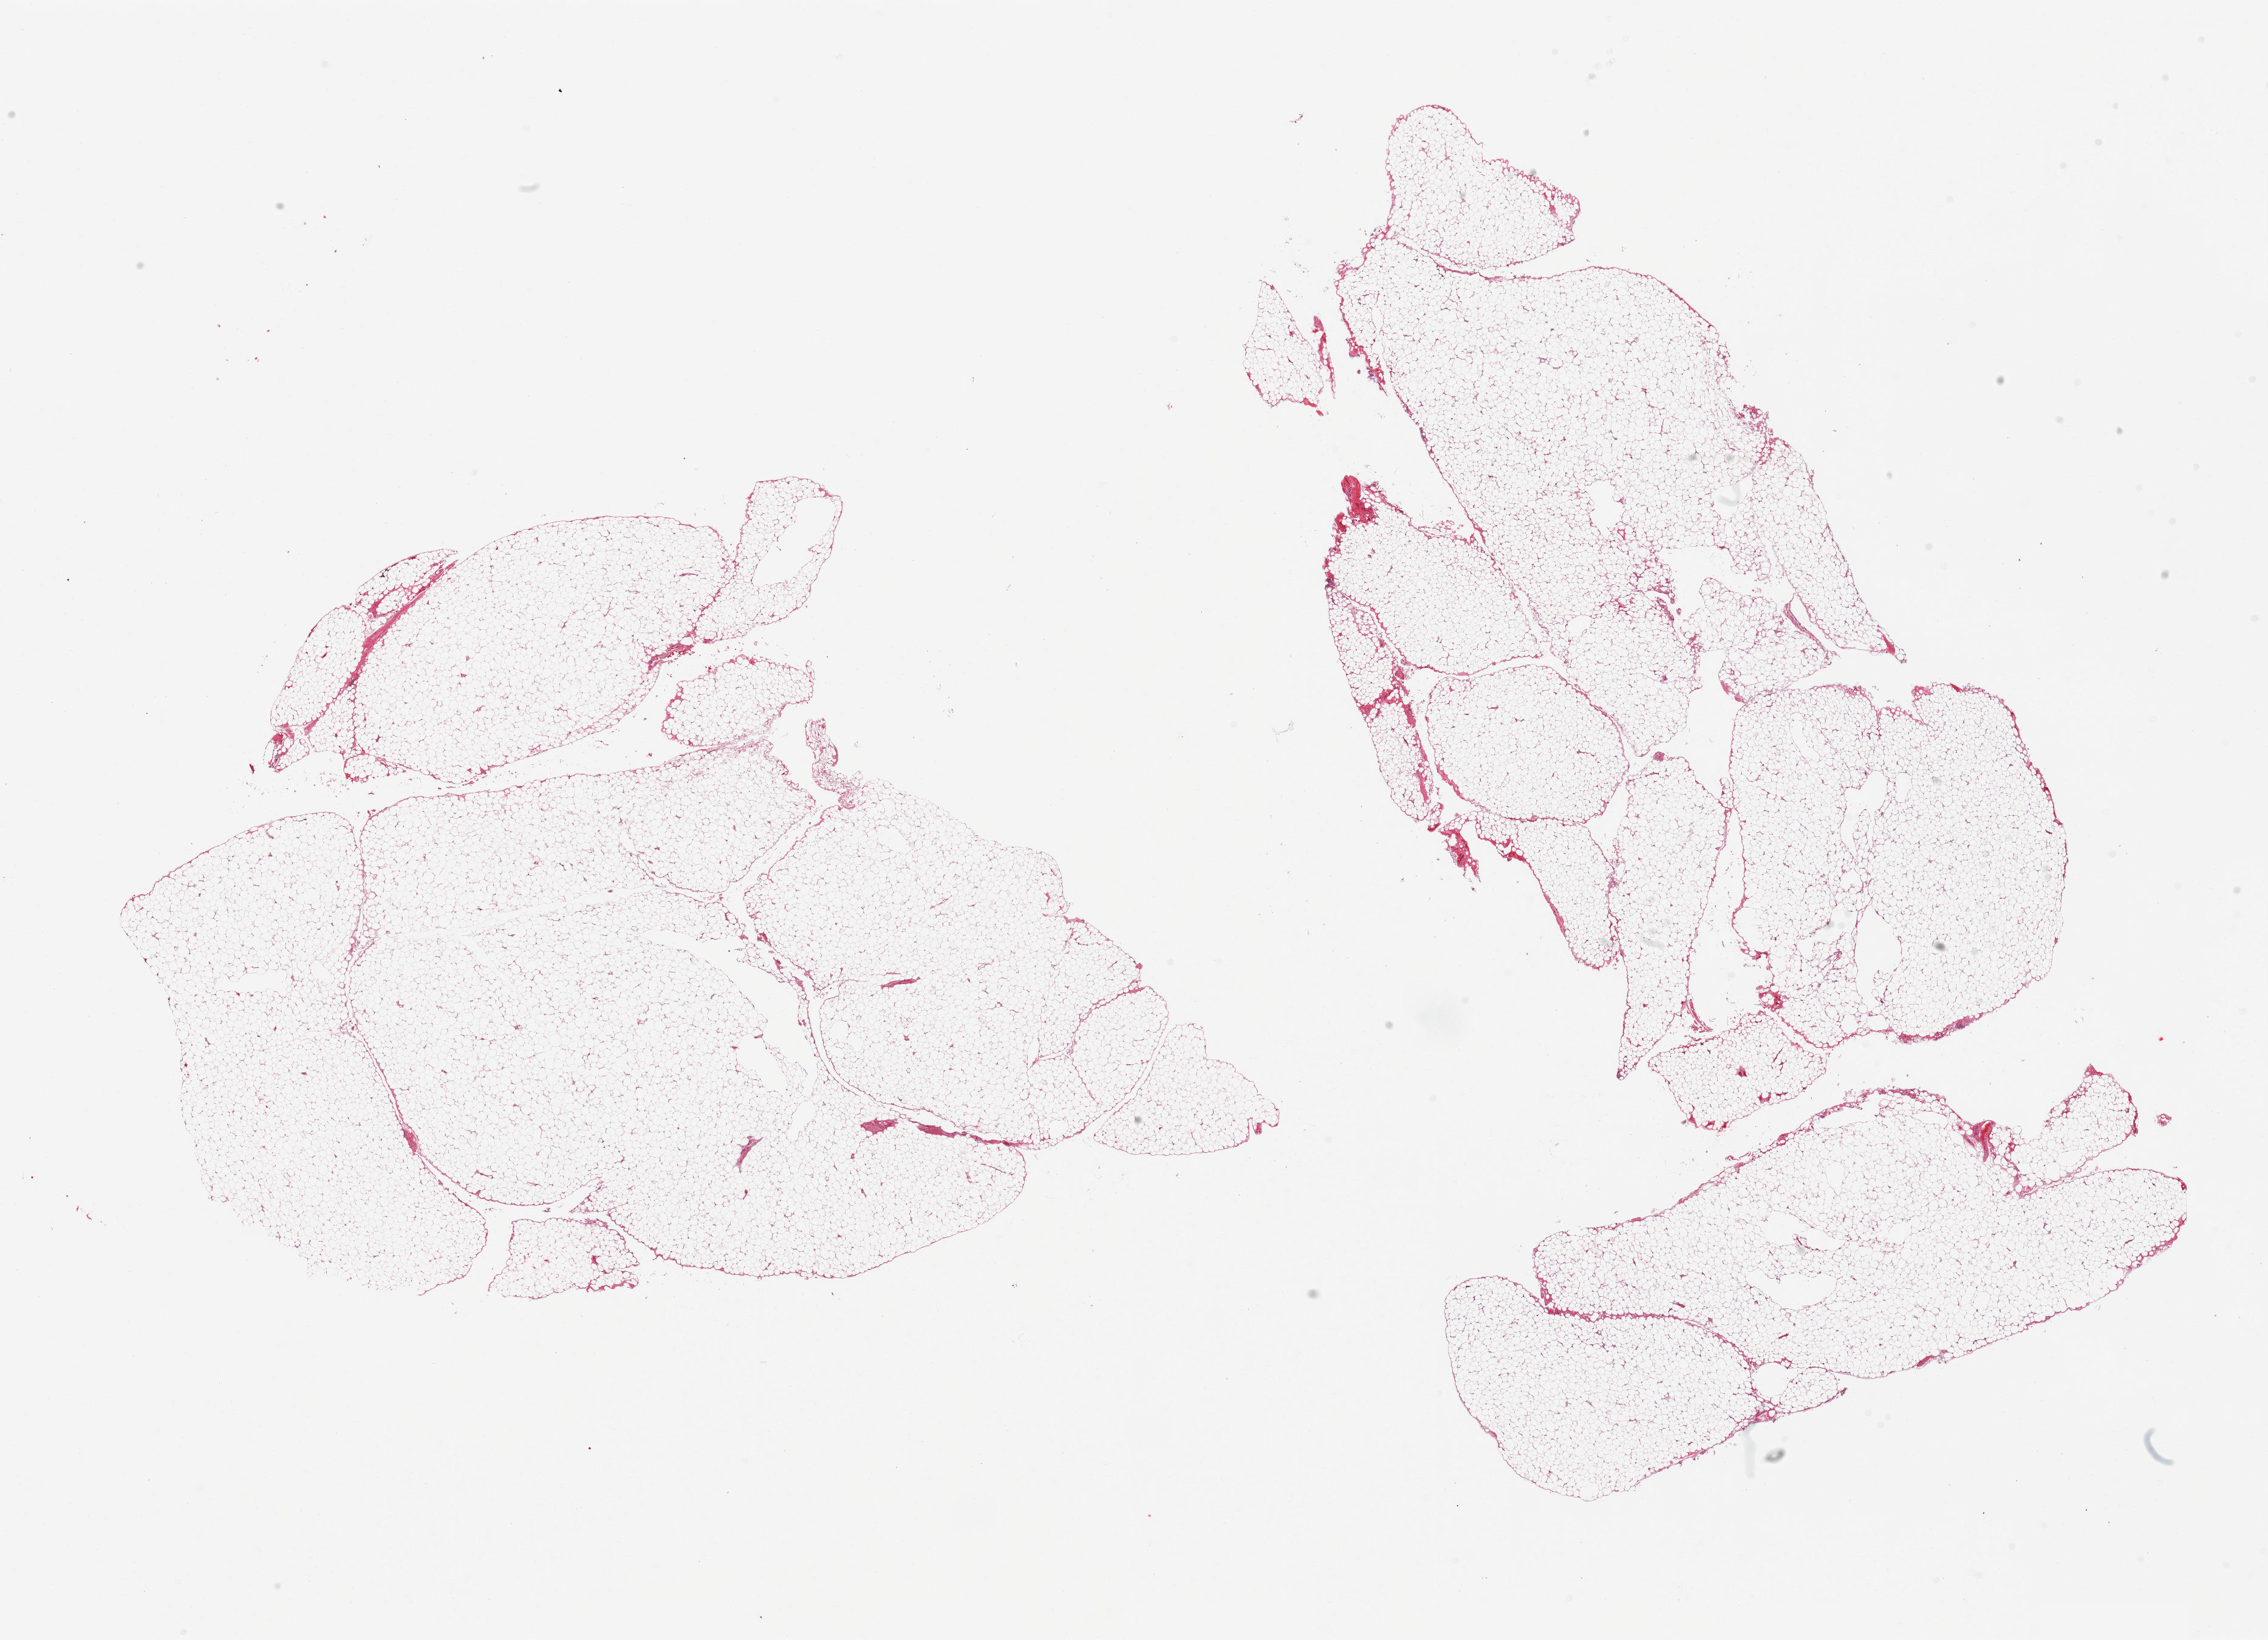
Haematoxylin and eosin whole-slide image, shown as a low-resolution overview of the whole scanned area (about 29.5 x 21.4 mm), PAXgene-fixed, paraffin-embedded tissue, sampled site (target tissue): omentum, tissue donor sample. Male donor.
Pathologist's review note for this sample: 2 pieces.